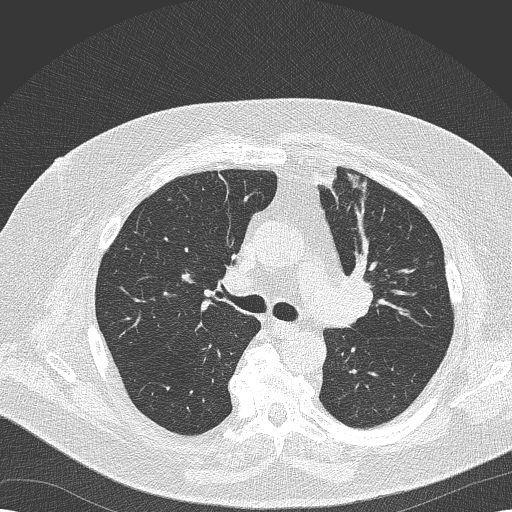
Low-dose screening chest CT, axial slice, second annual screen, lung window (W 1500 / L -600 HU), 512 × 512 image matrix, field of view 370 × 370 mm. Male participant, aged 68 years at enrolment. Former smoker at enrolment.
• Expert reader's lesion annotation, bounding box <322,267,378,330> (left, top, right, bottom; pixels).
• Reader record for this screening exam (exam-level; its link to the box is not recorded): non-calcified nodule or mass ≥4 mm, left lower lobe, 8 × 6 mm, soft tissue attenuation, pre-existing on the prior screen: yes; interval growth: no.
• Later outcome: lung cancer diagnosed 256 days after this screen — squamous cell carcinoma, NOS, left upper lobe, poorly differentiated (G3), stage IIB (AJCC 6th edition), 35 mm at pathology.